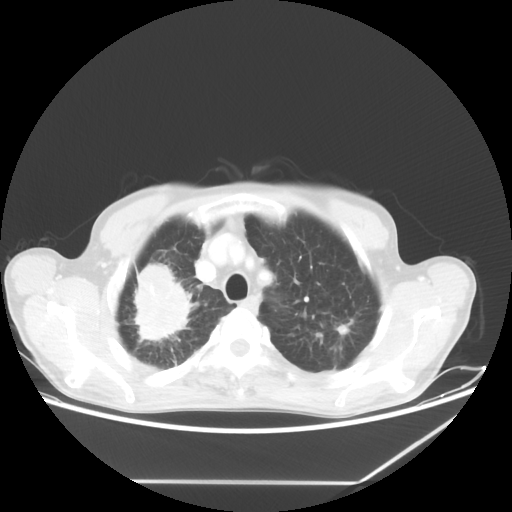
Chest CT, one axial slice. Position 52 of 65 along the scan axis. Reconstruction kernel STANDARD. Lung window (W 1500 / L -600 HU). 5 mm slice thickness. 512 × 512 image matrix. Male patient, age 68 years. From the clinical record (not read from this slice): clinical TNM (as recorded): T3 N3 M0.
Outlined on this slice (bounding box drawn by a radiologist):
- lung tumour (recorded histology: adenocarcinoma): bounding box <112,256,216,363> (left, top, right, bottom; pixels)